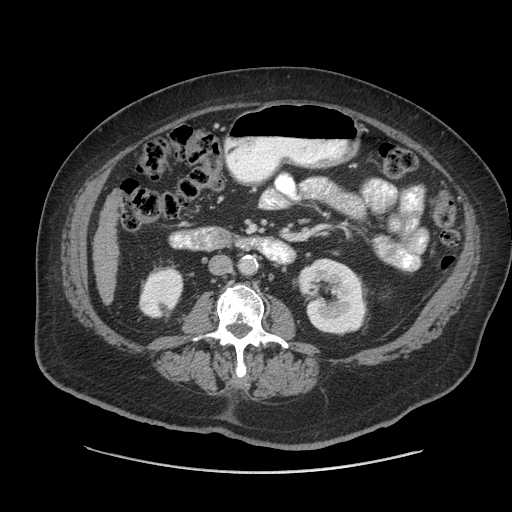
Contrast-enhanced abdominal CT (liver protocol), one axial slice. Position 13 of 91 along the scan axis. Reconstruction kernel STANDARD. 140 kVp. Soft-tissue window (W 400 / L 40 HU). 2.5 mm slice thickness. 512 × 512 image matrix. From the clinical record (not read from this slice): diagnosis: hepatocellular carcinoma (patient treated with transarterial chemoembolisation; whether this scan precedes or follows treatment is not stated here); TNM stage (as recorded): Stage-I; Child-Pugh class: A.
Outlined on this slice (semi-automatic segmentation, software-assisted and operator-edited):
- liver parenchyma outside the tumour (the mass and vessels are separate outlines, so this box may not span the whole liver): bounding box (x1, y1, x2, y2) in pixels: (92, 194, 118, 303)